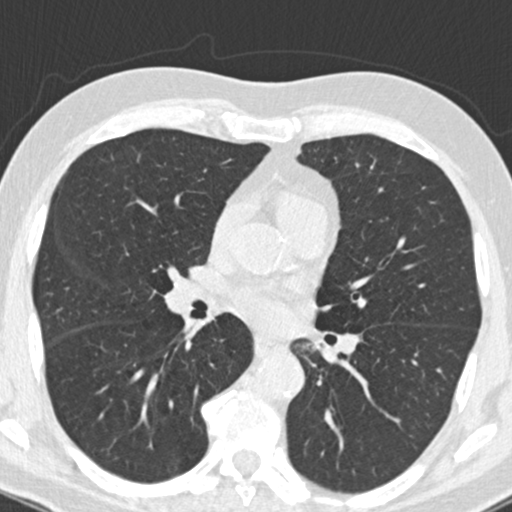
Chest CT (low-dose screening protocol), one axial image; second screening round (one year after baseline); lung window (W 1500 / L -600 HU). Male, age 66 years at enrolment.
Lesion marked by an expert reader, bounding box <182,313,210,341> (left, top, right, bottom; pixels). Screening reader's record for this exam (one nodule recorded; not confirmed to be the boxed lesion): non-calcified nodule or mass ≥4 mm, right upper lobe, 5 × 4 mm, smooth margins, pre-existing on the prior screen: yes; interval growth: no. Participant outcome: lung cancer diagnosed 403 days after this screen — squamous cell carcinoma, NOS, right lower lobe, poorly differentiated (G3), stage IIA (AJCC 6th edition), 22 mm at pathology.